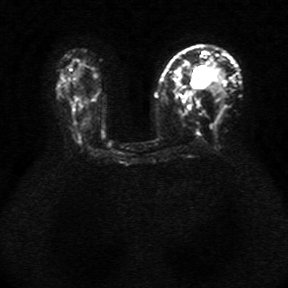
Breast MRI, one axial slice; position 18 of 34 along the scan axis; diffusion-weighted series; image 2 of 4 stored at this slice position (different b-values; order by instance number); 1.5 T; 5 mm slice thickness; 288 × 288 image matrix, field of view 340 × 340 mm. Female patient.
Outlined on this slice (expert manual segmentation):
- tumour on diffusion-weighted imaging: box from (x=192, y=70) to (x=210, y=87) px